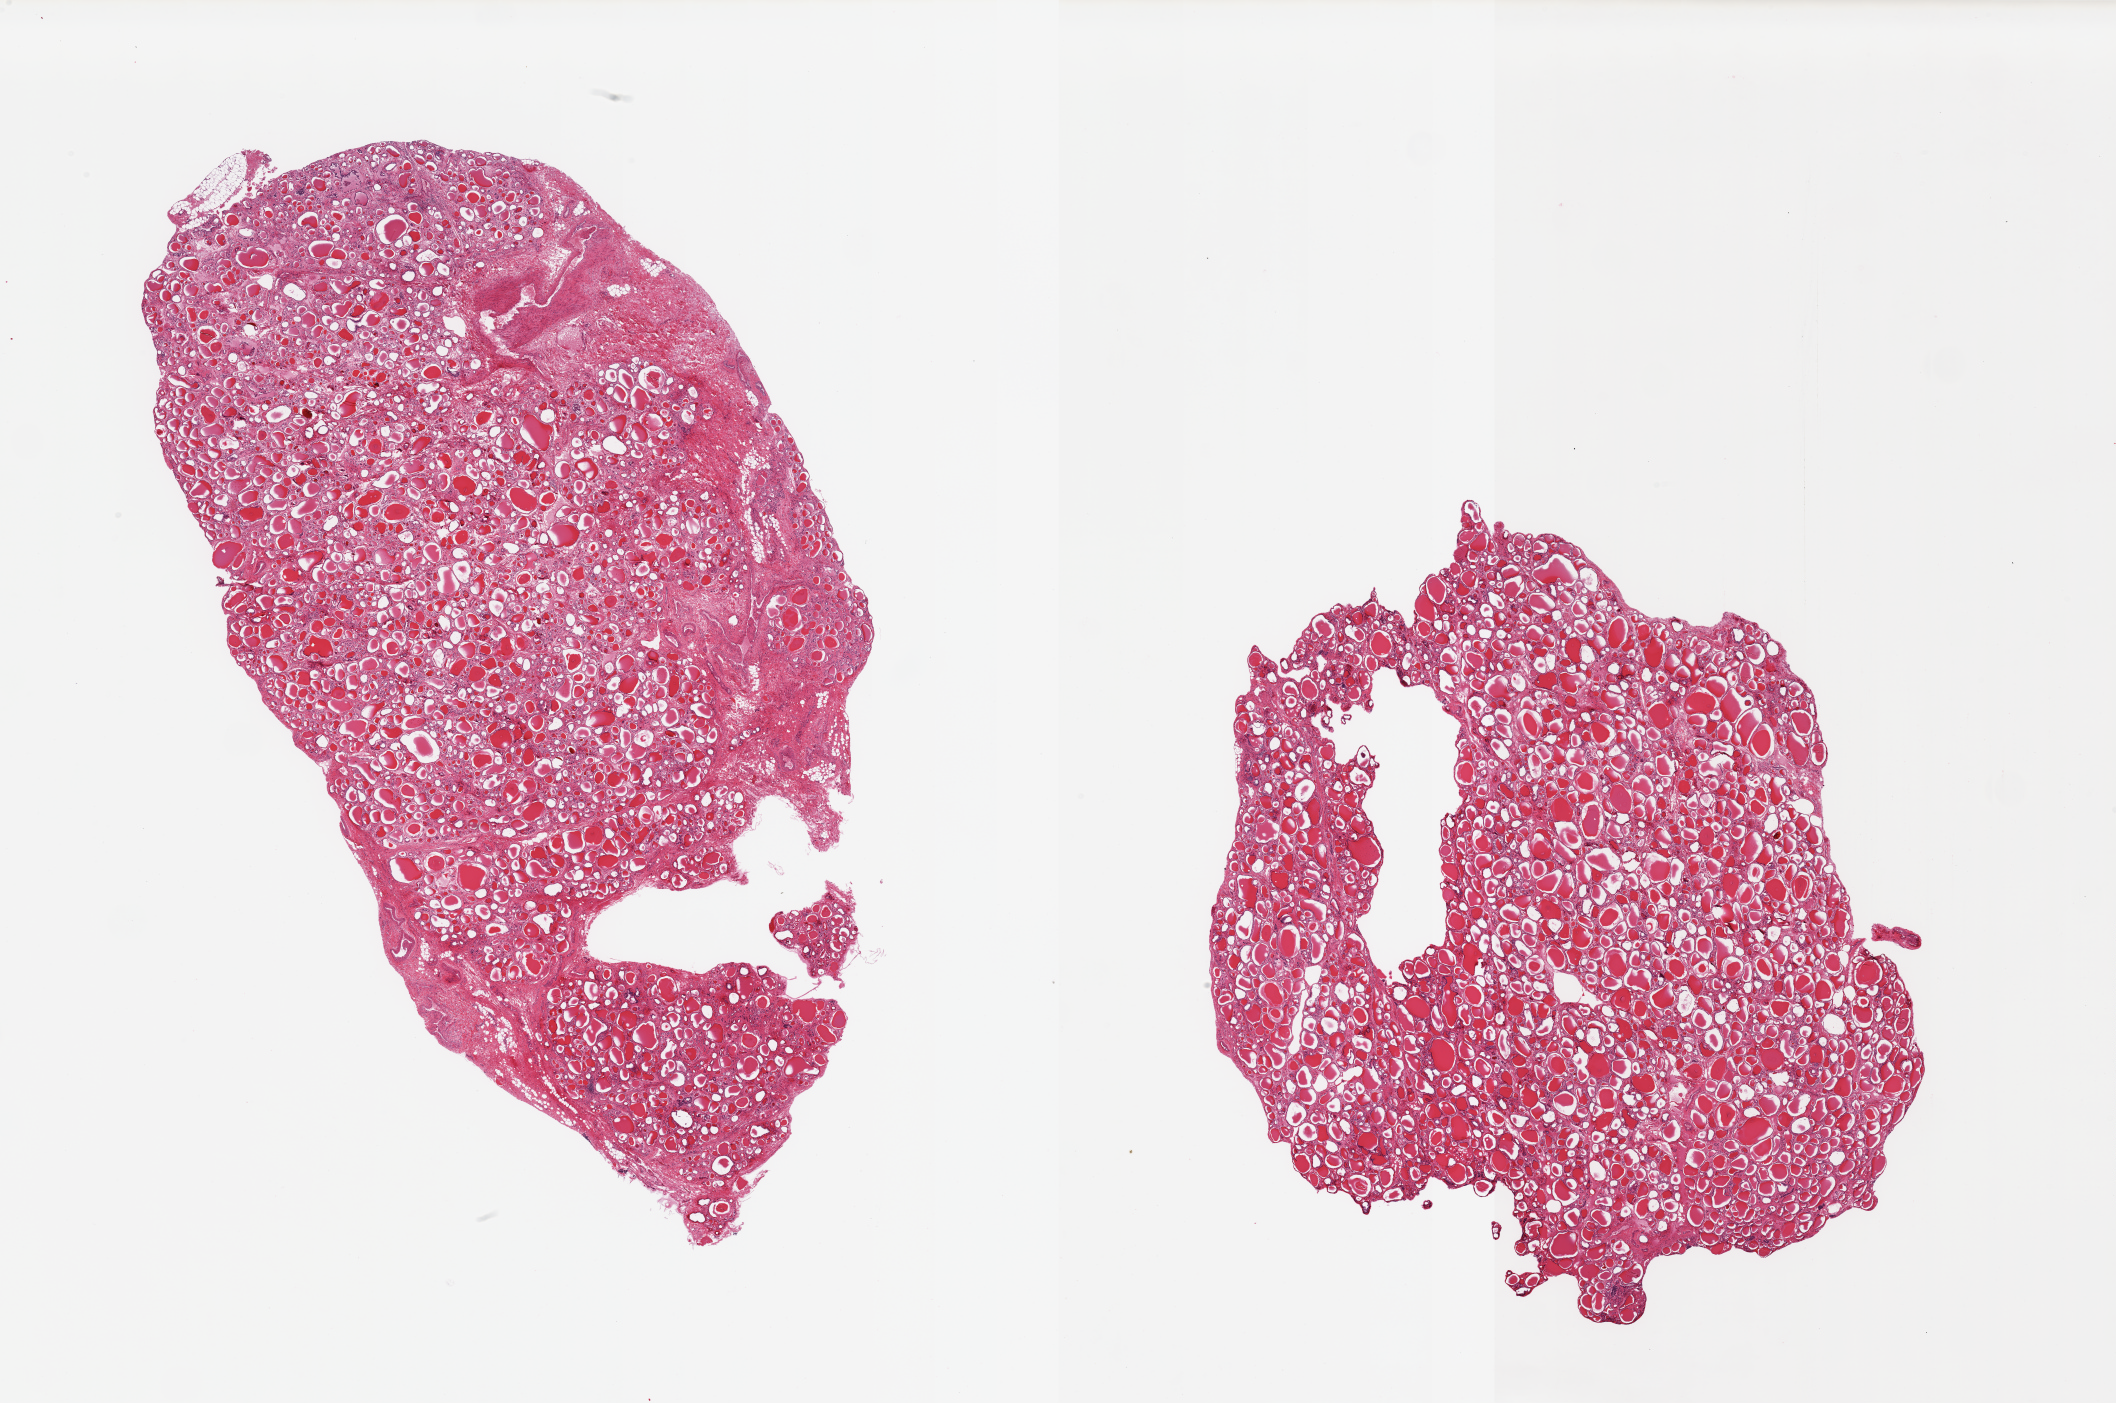
Digitized H&E-stained section, low-resolution overview of the scanned area, about 33.5 x 22.2 mm (acquisition: 20x scan); PAXgene-fixed, paraffin-embedded tissue; section of thyroid (target tissue); tissue donor sample. Donor: male.
* reviewer comment on this tissue sample: 2 pieces; 10% stromal & vascular content in 1 piece